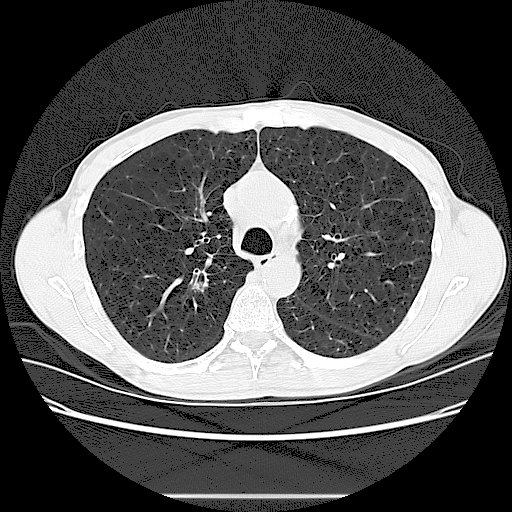
Low-dose screening chest CT, axial slice, second screening round (one year after baseline), lung window (W 1500 / L -600 HU), 2.5 mm slice thickness, lung (sharp) reconstruction kernel (LUNG), slice 42 of 131 in the series. Male, age 59 years at enrolment. Current smoker at enrolment.
Lesion marked by an expert reader, bounding box <177,266,220,309> (left, top, right, bottom; pixels). The exam's reader record, not a measurement of the box and not confirmed to be the same lesion: non-calcified nodule or mass ≥4 mm, right upper lobe, 7 × 4 mm, smooth margins, soft tissue attenuation, pre-existing on the prior screen: no. Lung cancer was diagnosed 69 days after this screen: squamous cell carcinoma, NOS, right upper lobe, stage IIIA (AJCC 6th edition), 7 mm at pathology.